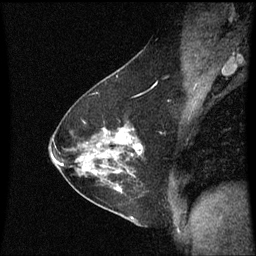
Breast MRI (dynamic contrast-enhanced), one sagittal slice. Slice 38 of 60 in the series (ordered by position). Dynamic contrast-enhanced series, image 2 of 3 at this slice position (ordered by acquisition). 1.5 T. TE 4.2 ms, TR 8.9 ms. 2 mm slice thickness. 256 × 256 image matrix, field of view 200 × 200 mm. Female patient, age 54 years. From the clinical record (not read from this slice): setting: breast cancer imaged before/during neoadjuvant chemotherapy; receptor status: HER2-positive.
Outlined on this slice (semi-automatically segmented with operator editing):
- analysis volume of interest (the breast-tissue region the enhancement analysis was run in; not a lesion): box from (x=102, y=122) to (x=144, y=169) px
- tumour enhancement mask (voxels above the 70 % enhancement threshold inside the analysis volume of interest): (x=115, y=132)–(x=142, y=155)